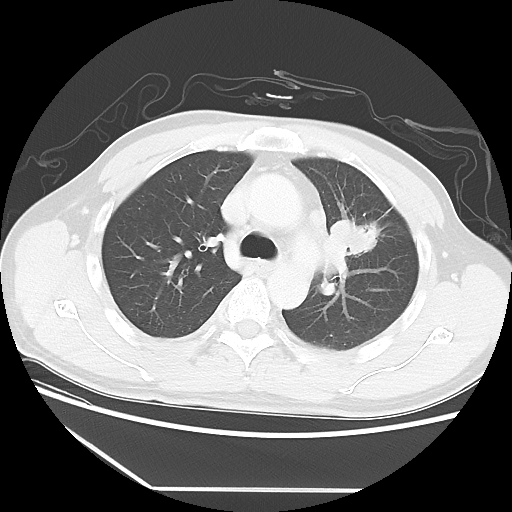
Chest CT, one axial slice. Position 38 of 56 along the scan axis. 120 kVp. Lung window (W 1500 / L -600 HU). 5 mm slice thickness. 512 × 512 image matrix, field of view 373 × 373 mm. Patient: male, 53 years. Case-level facts recorded for this patient, not image findings: clinical TNM (as recorded): T2a N1 M1b.
Outlined on this slice (rectangle marked by the reading radiologist):
- lung tumour (recorded histology: adenocarcinoma): bounding box (x1, y1, x2, y2) in pixels: (334, 206, 383, 263)